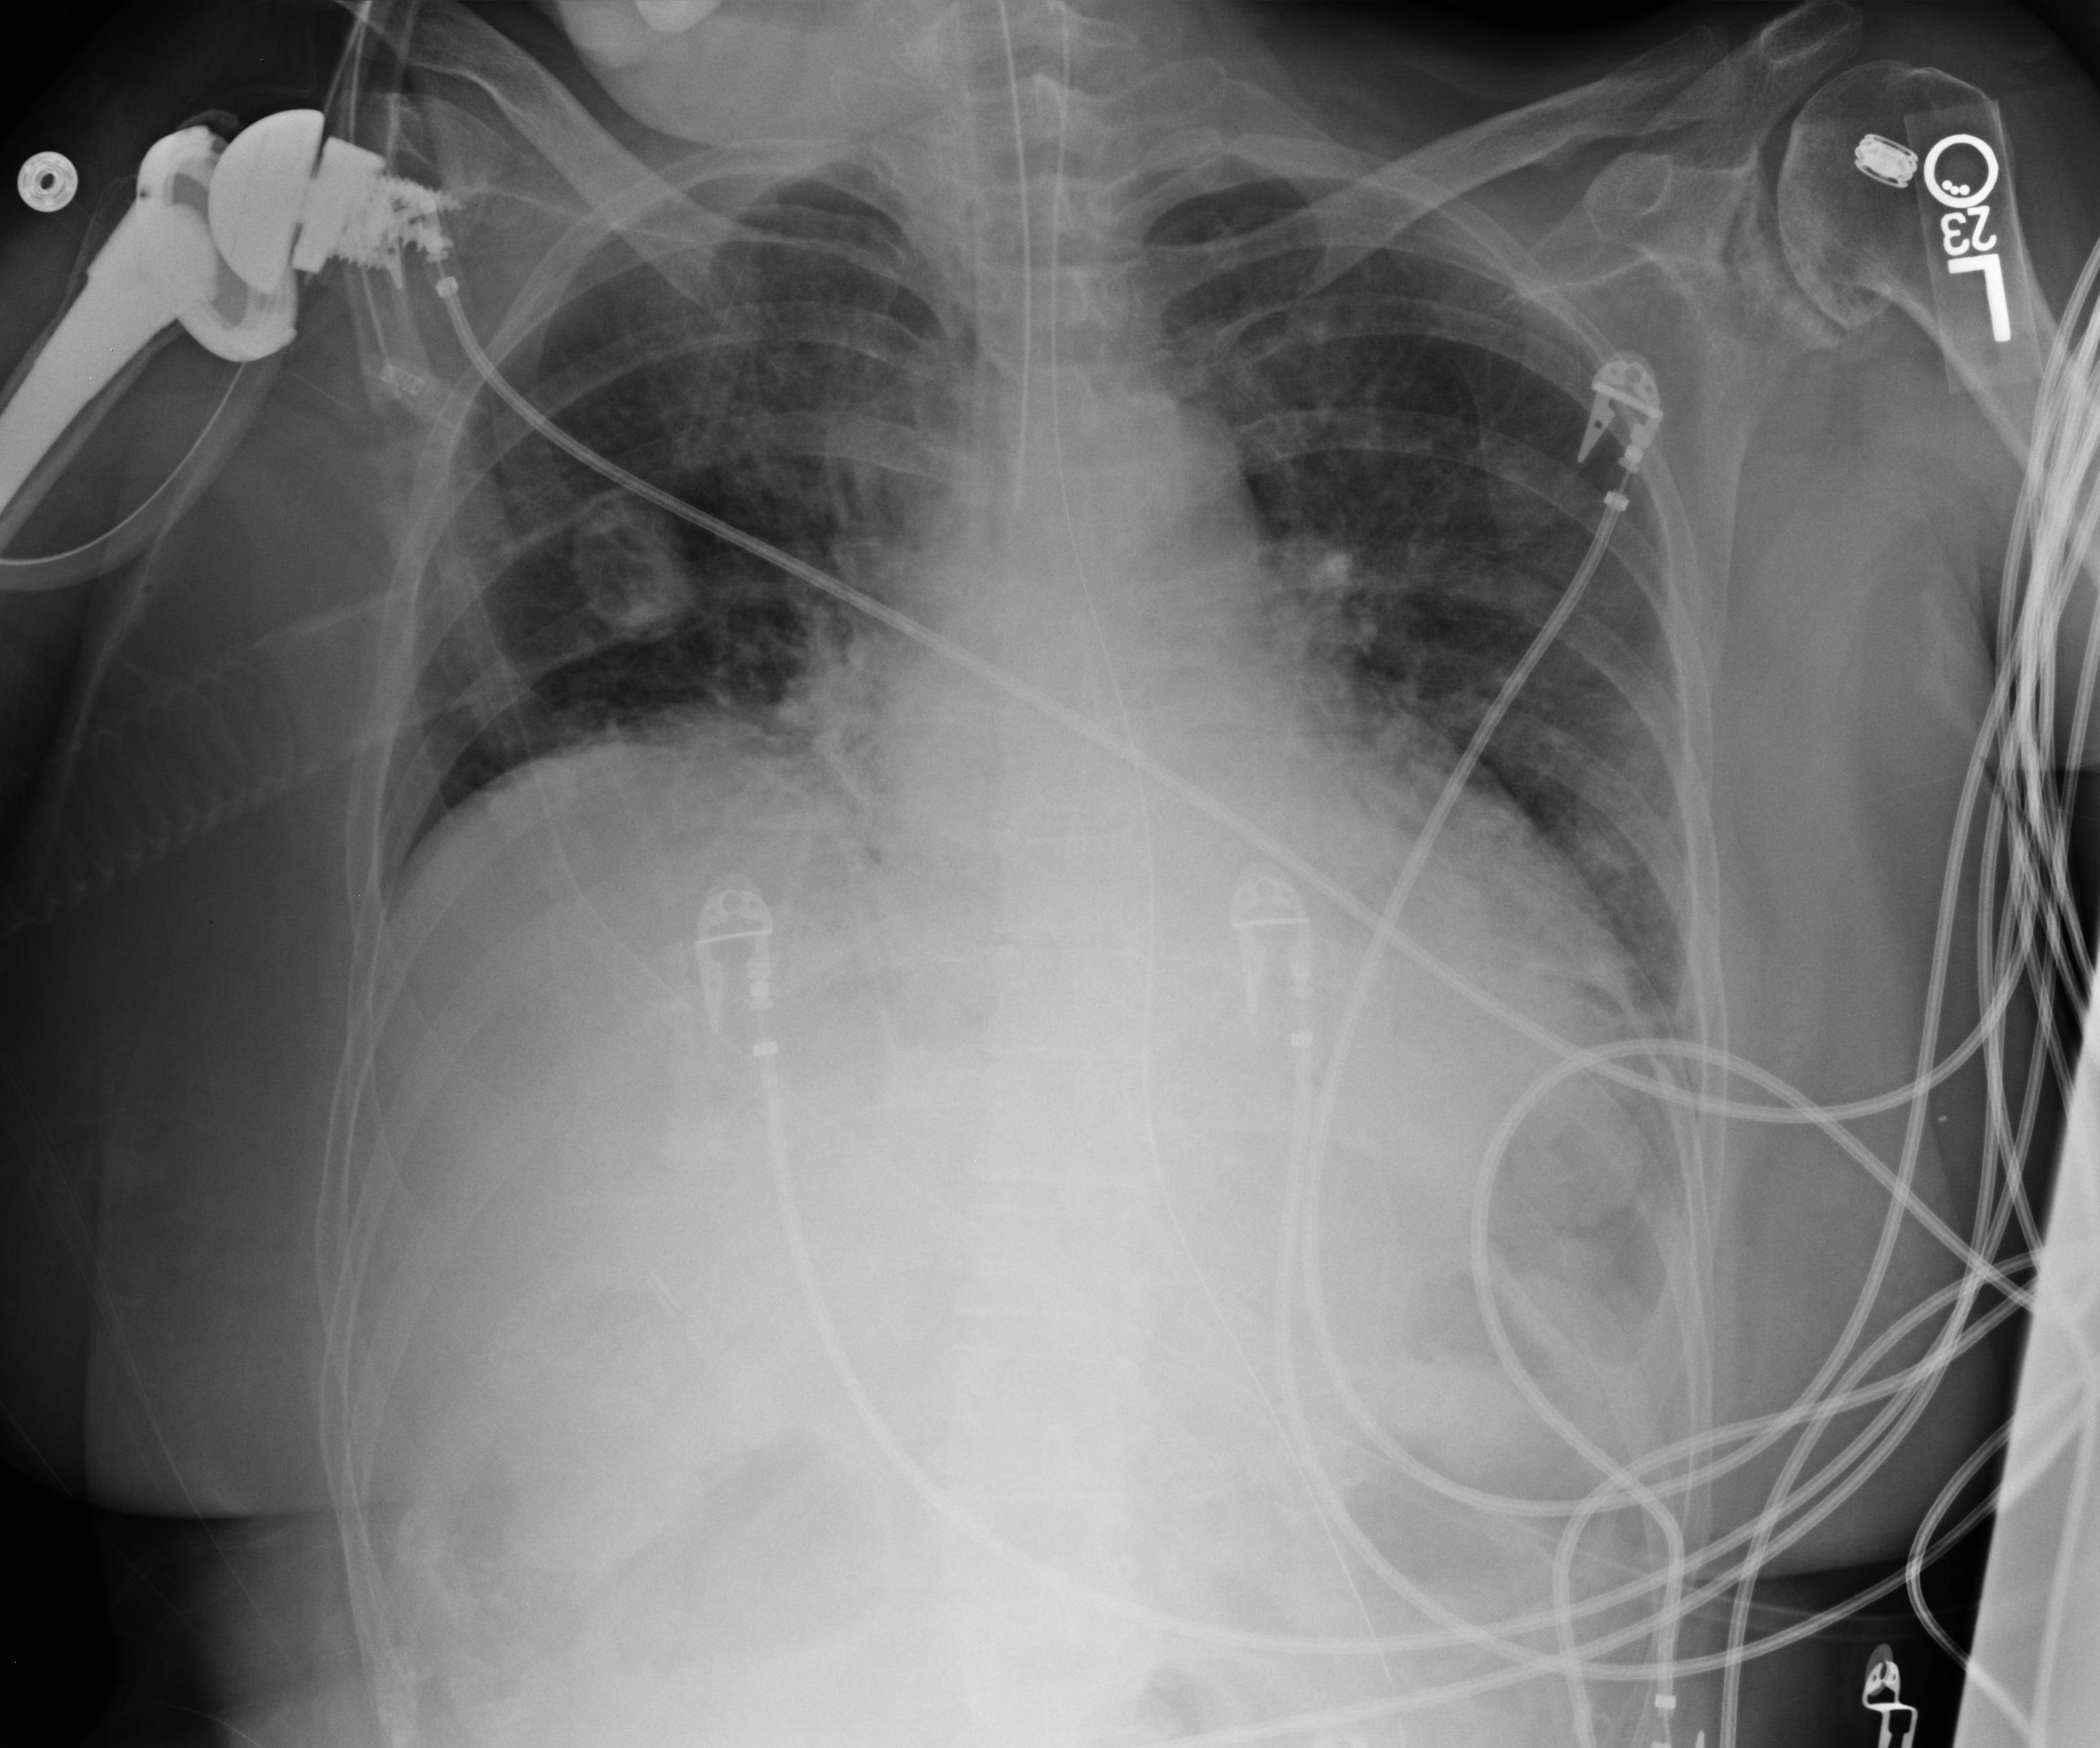
Chest X-ray (portable); anteroposterior (AP) projection. Patient hospitalised with COVID-19; female, aged 60–74 years.
Admission-level facts for this patient (not findings on this image; timing relative to this image not recorded): mechanically ventilated during this hospital stay: yes; length of hospital stay: 27 days.